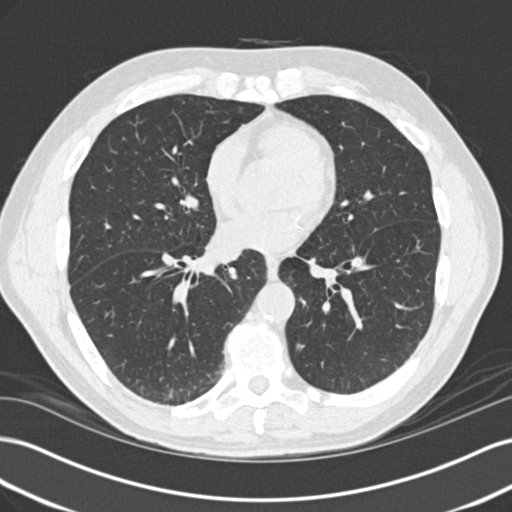
Low-dose screening chest CT, axial slice; baseline screening round; lung window (W 1500 / L -600 HU); 2 mm slice thickness; 512 × 512 image matrix. Male participant, aged 64 years at enrolment. Former smoker at enrolment.
Lesion marked by an expert reader, bounding box [x1, y1, x2, y2] px = [275, 331, 319, 372]. Screening reader's record for this exam: no non-calcified nodule ≥4 mm recorded. Lung cancer was diagnosed 844 days after this screen (after the third annual screen): adenocarcinoma with mixed subtypes, left lower lobe, well differentiated (G1), stage IA (AJCC 6th edition), 7 mm at pathology.